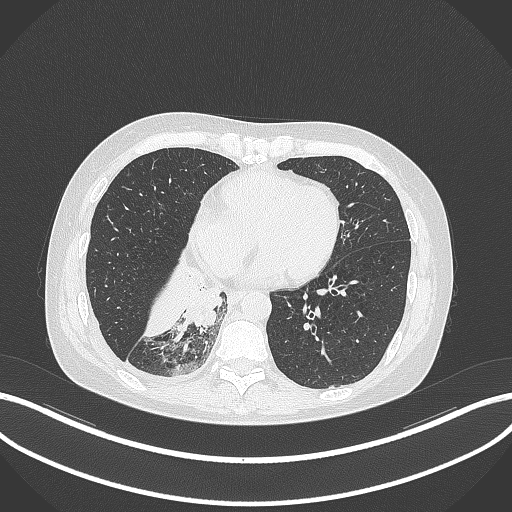
Chest CT, one axial slice. Position 106 of 329 along the scan axis. Reconstruction kernel B70f. 120 kVp. Lung window (W 1500 / L -600 HU). 512 × 512 image matrix, field of view 400 × 400 mm. Female patient, age 63 years. From the clinical record (not read from this slice): clinical TNM (as recorded): T1c N0 M0.
Structures marked on this image (rectangle marked by the reading radiologist):
- lung tumour (recorded histology: adenocarcinoma): box from (x=180, y=278) to (x=224, y=328) px